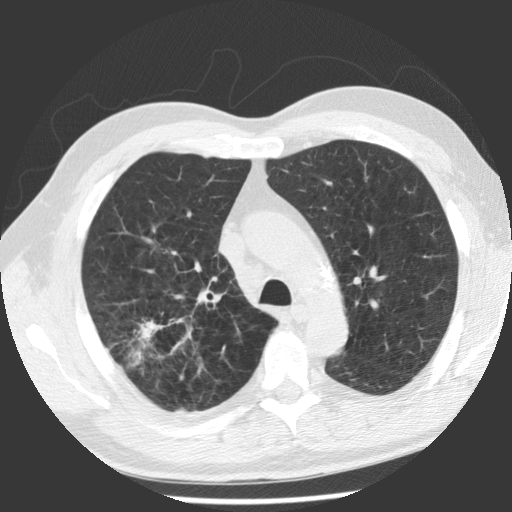
Axial slice from a low-dose chest CT screening exam, baseline annual screen, lung window (W 1500 / L -600 HU), standard (soft-tissue) reconstruction kernel (STANDARD), 140 kVp, slice 79 of 112 in the series. Male participant, aged 62 years at enrolment. Former smoker at enrolment.
Expert reader's lesion annotation, bounding box [x1, y1, x2, y2] px = [110, 300, 185, 373]. The screening reader recorded 2 non-calcified nodules or masses ≥4 mm on this exam (right upper lobe, right upper lobe); which of them this box marks is not recorded. Participant outcome: lung cancer diagnosed 71 days after this screen — adenocarcinoma, NOS, right upper lobe, poorly differentiated (G3), stage IV (AJCC 6th edition), 30 mm at pathology.